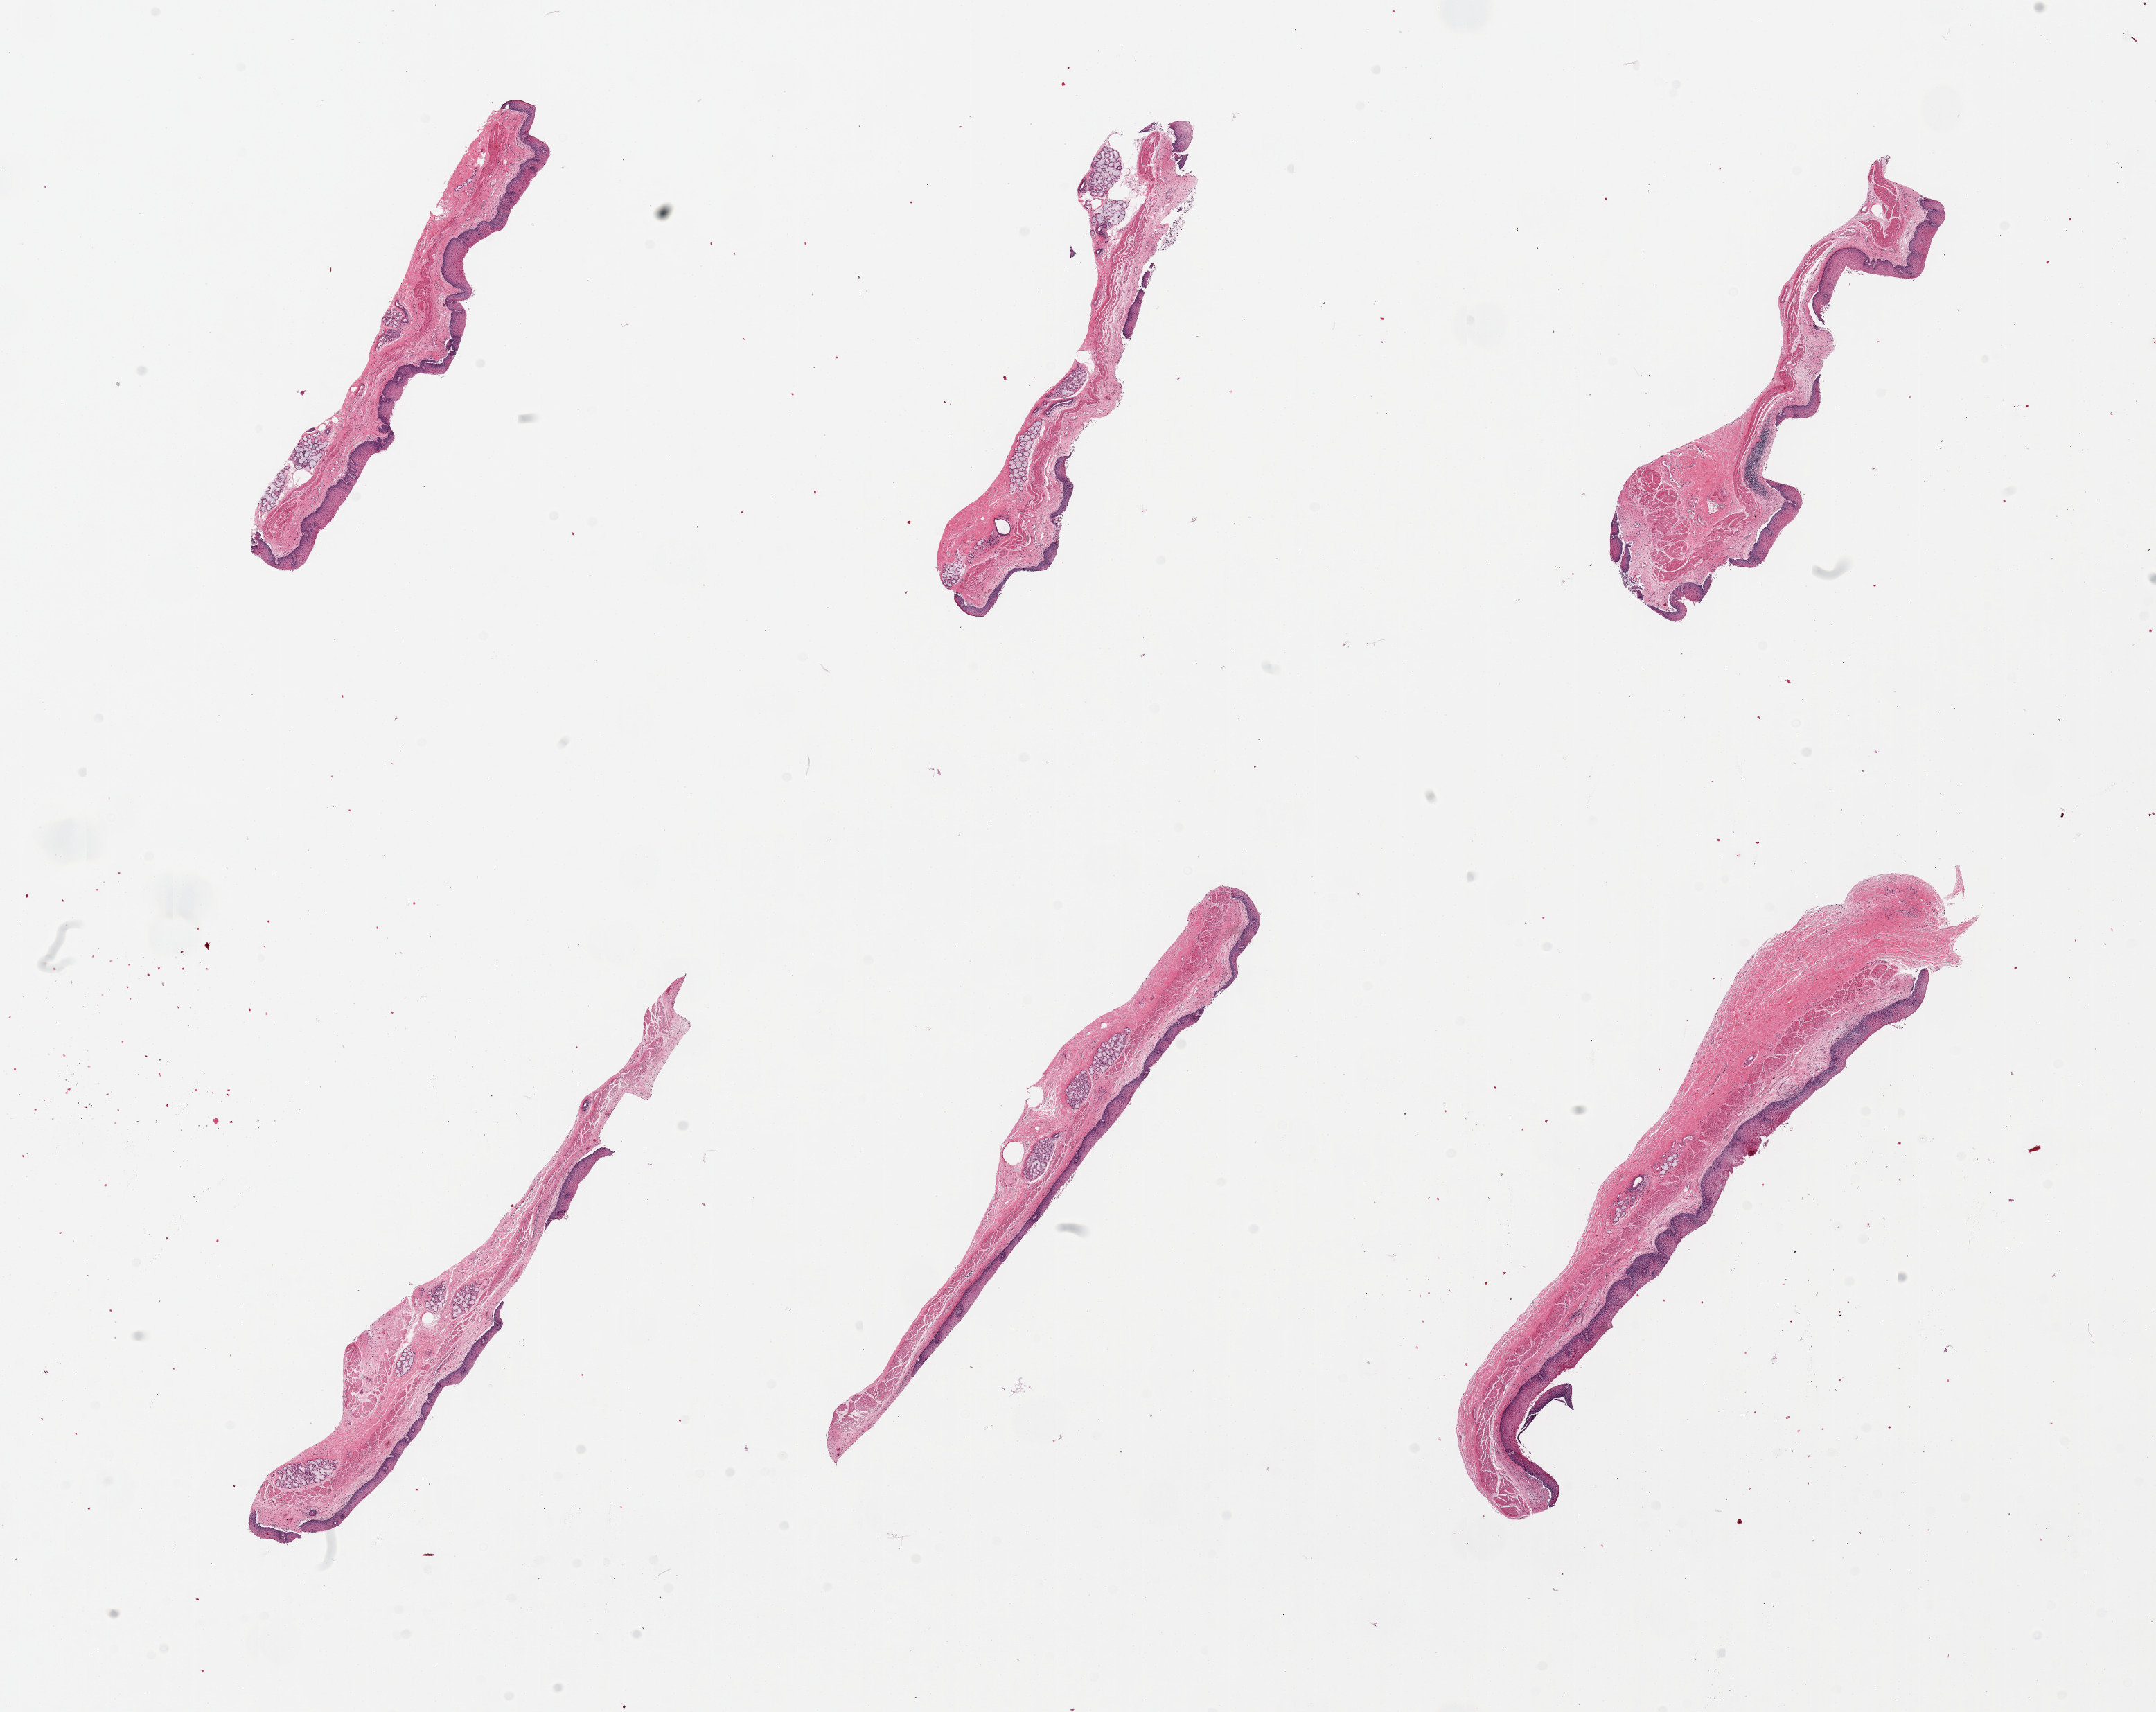
Whole-slide image, haematoxylin and eosin stain, brightfield, low-resolution overview of the scanned area, about 24.6 x 19.5 mm (acquisition: 20x scan); PAXgene-fixed paraffin-embedded (PFPE) section; target tissue: esophageal mucous membrane; tissue donor sample. Donor sex: male.
Reviewer comment on this tissue sample: 6 pieces, all with mucosa, focal chronic inflammation.